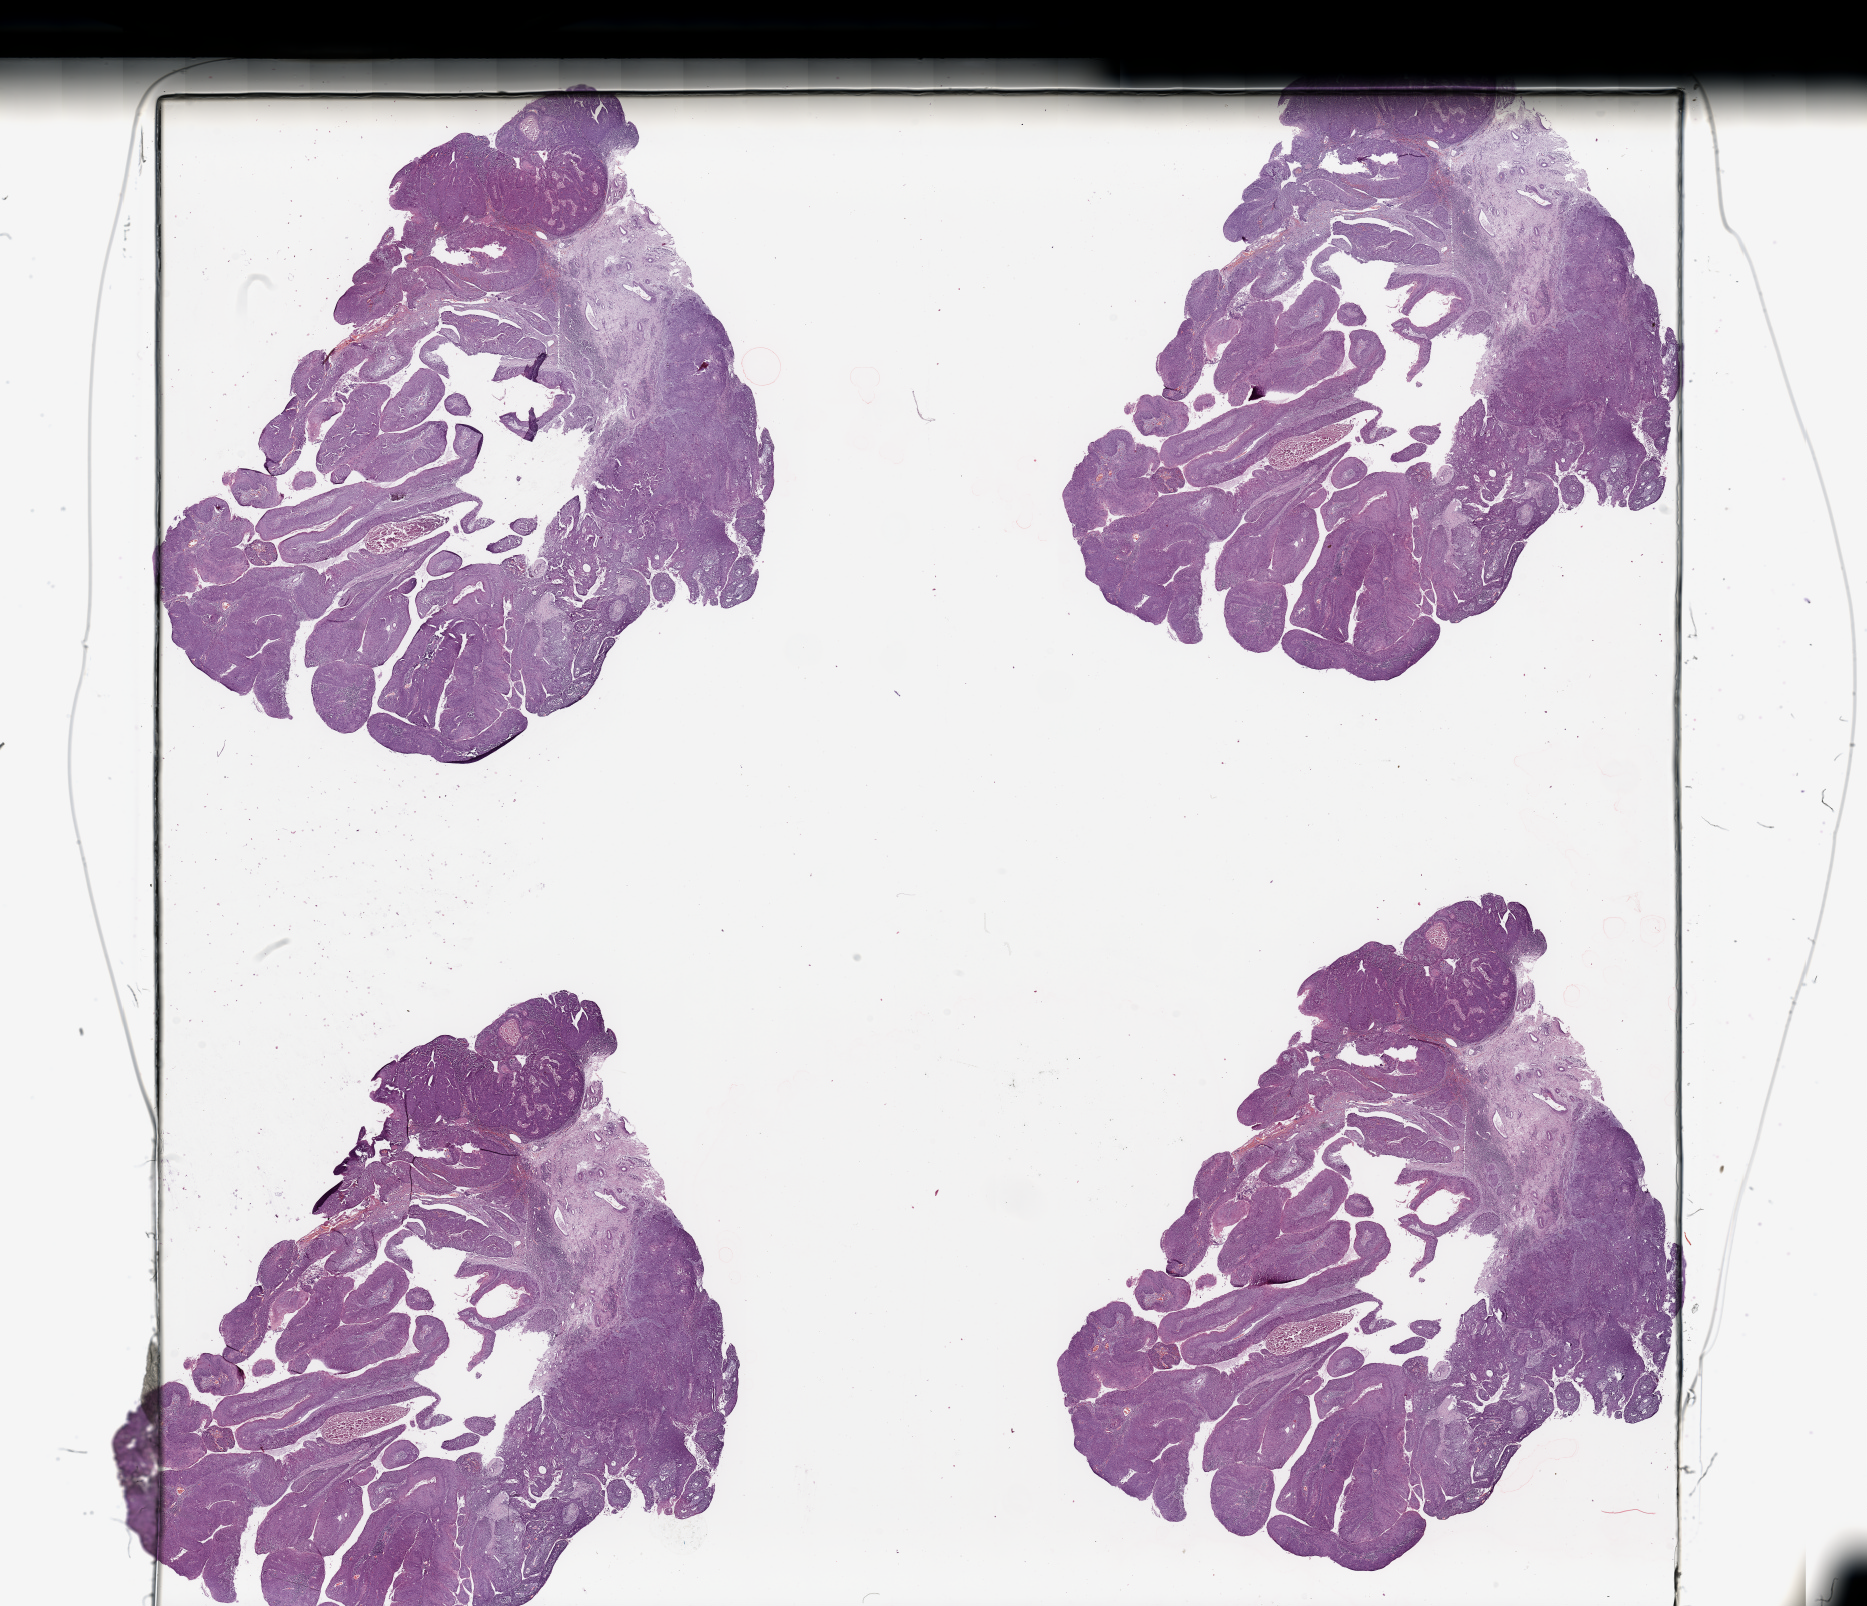
H&E-stained whole-slide image, low-resolution overview of the scanned area, about 29.5 x 25.4 mm, tumour tissue sample, sampled site: oropharynx. Patient: male, age 54 years. Histologic grade: G2 (moderately differentiated). Pathologist review of this section (percent, as recorded): tumour nuclei 90%, necrosis 5%.
• diagnosis: Squamous cell carcinoma, NOS
• primary tumour site (as recorded): oropharynx
• AJCC pathologic stage: IVA